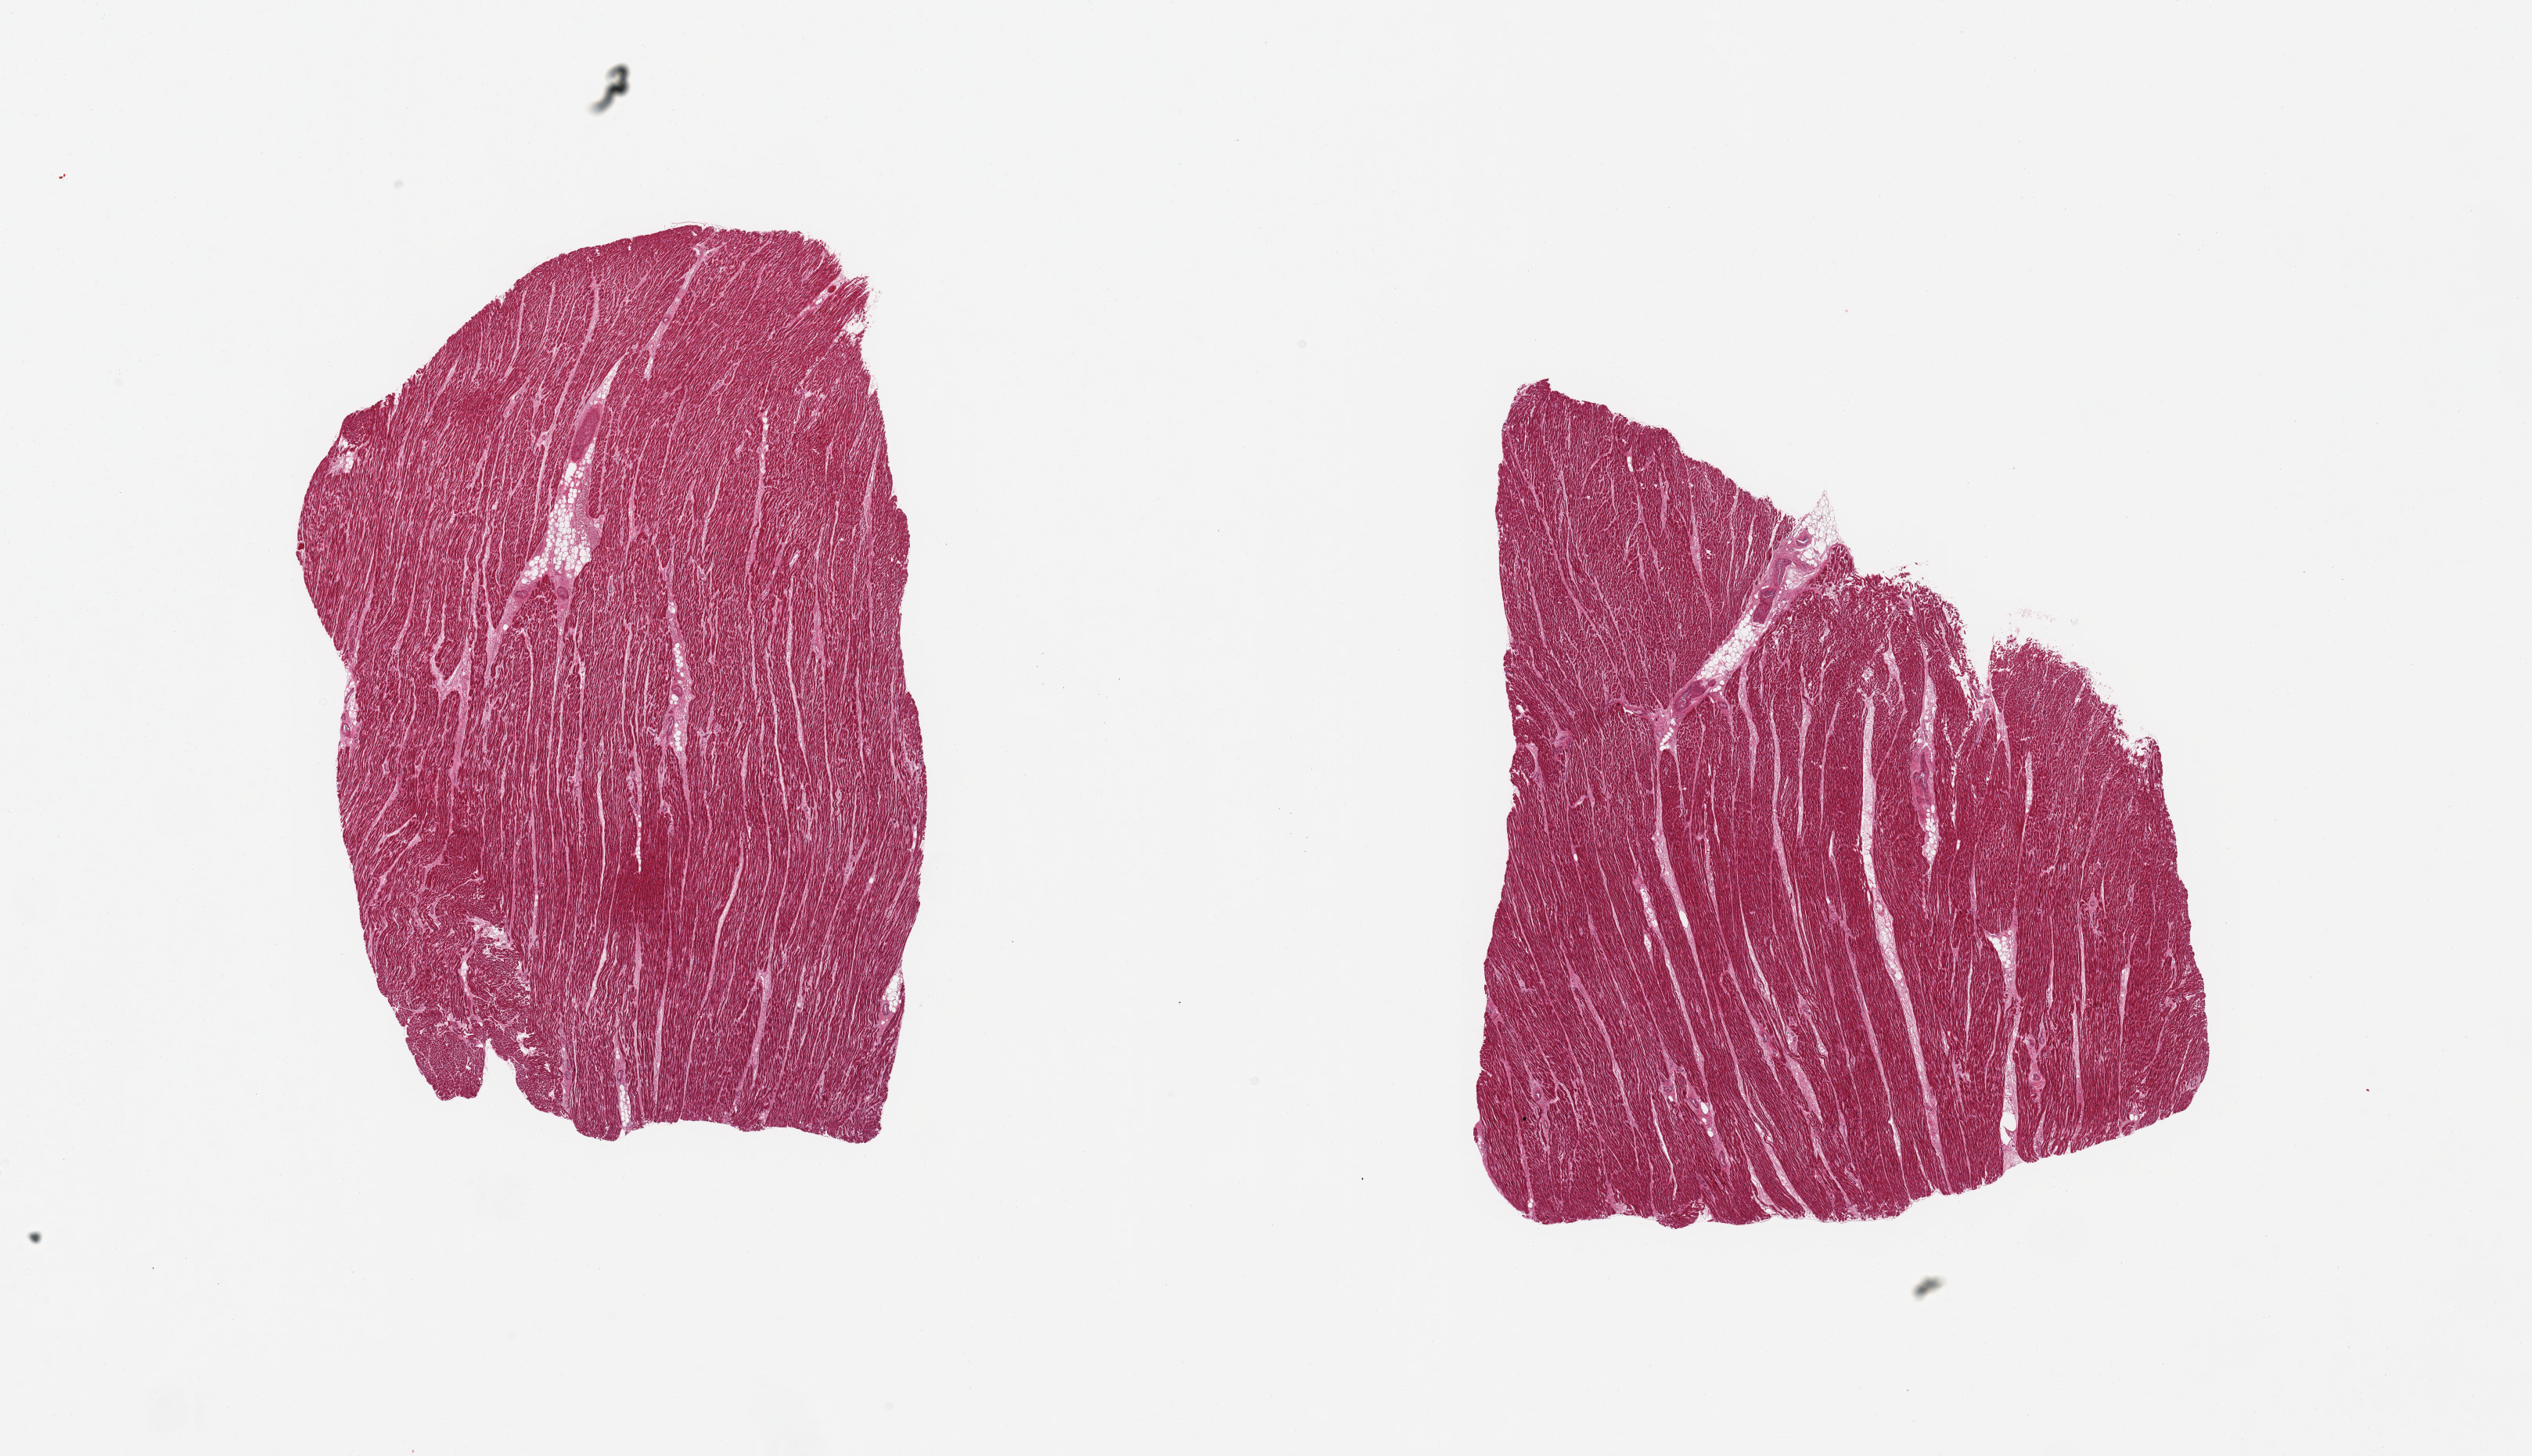
Whole-slide image, hematoxylin and eosin (H&E) stain, shown as a low-resolution overview of the whole scanned area (about 25.6 x 14.7 mm); PAXgene-fixed paraffin-embedded (PFPE) section; sampled site (target tissue): heart; donor tissue sample. Female donor.
Reviewer comment on this tissue sample: 2 pieces.